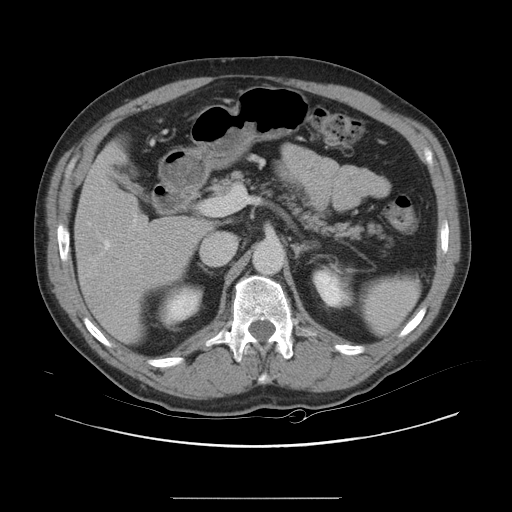
Contrast-enhanced abdominal CT, one axial slice; position 12 of 40 along the scan axis; 120 kVp; intravenous contrast given; soft-tissue window (W 400 / L 40 HU); 5 mm slice thickness; 512 × 512 image matrix, field of view 408 × 408 mm. Male patient, age 64 years. Case-level facts recorded for this patient, not image findings: diagnosis: colorectal cancer liver metastases, imaged before liver resection; multiple liver metastases: yes; largest metastasis: 3.2 cm; disease in both lobes: yes.
Structures marked on this image (expert manual segmentation):
- hepatic veins: bounding box <104,241,110,249> (left, top, right, bottom; pixels)
- liver: <75,147,205,342>
- planned liver remnant (the part of the liver to remain after resection): <89,147,206,234>